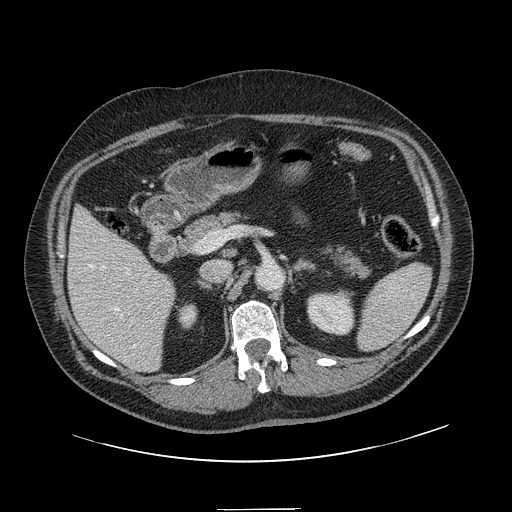
Contrast-enhanced abdominal CT, one axial slice. Position 71 of 154 along the scan axis. Intravenous contrast given. Soft-tissue window (W 400 / L 40 HU). 512 × 512 image matrix, field of view 451 × 451 mm. Male patient, age 61 years. From the clinical record (not read from this slice): diagnosis: colorectal cancer liver metastases, imaged before liver resection; multiple liver metastases: yes; largest metastasis: 2.6 cm; chemotherapy before resection: no.
Structures marked on this image (outlined manually by an expert reader):
- hepatic veins: box from (x=88, y=264) to (x=135, y=349) px
- liver: (x=69, y=209)–(x=174, y=371)
- planned liver remnant (the part of the liver to remain after resection): (x=70, y=209)–(x=174, y=366)
- portal vein (with intrahepatic branches): (x=131, y=320)–(x=133, y=322)
- liver metastasis: (x=77, y=282)–(x=81, y=287)